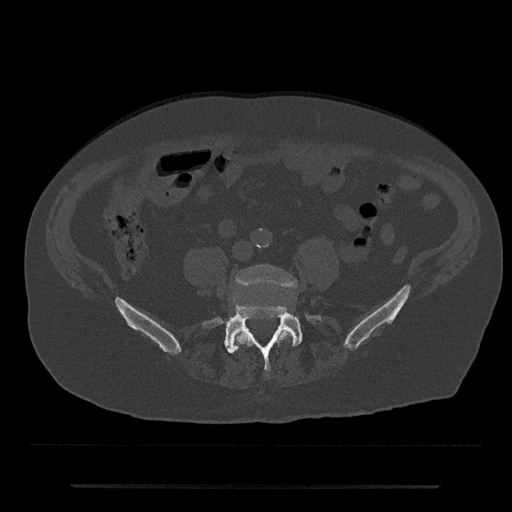
CT including the spine, one axial slice; position 309 of 797 along the scan axis; 120 kVp; bone window (W 1800 / L 400 HU); 0.5 mm slice thickness; 512 × 512 image matrix. Patient: male, 80 years. From the clinical record (not read from this slice): primary cancer: prostate; vertebrae with lytic lesions (as recorded): L1, T11.
Annotated regions visible in this slice (semi-automatic segmentation, software-assisted and operator-edited):
- L4 vertebra: bounding box <234,265,296,346> (left, top, right, bottom; pixels)
- L5 vertebra: <202,304,322,371>